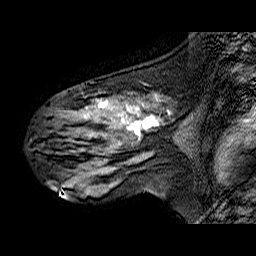
Breast MRI (dynamic contrast-enhanced), one sagittal slice. Slice 36 of 60 in the series (ordered by position). Dynamic contrast-enhanced series, time point 2 of 6 at this slice position (early post-contrast). 1.5 T. TE 6.3 ms, TR 32.9 ms. 4 mm slice thickness. 256 × 256 image matrix. Female patient. From the clinical record (not read from this slice): setting: breast cancer imaged before/during neoadjuvant chemotherapy; receptor status: HER2-positive.
Outlined on this slice (semi-automatic segmentation, software-assisted and operator-edited):
- analysis volume of interest (the breast-tissue region the enhancement analysis was run in; not a lesion): bounding box [x1, y1, x2, y2] px = [34, 90, 174, 173]
- tumour enhancement mask (voxels above the 100 % enhancement threshold inside the analysis volume of interest): [97, 100, 160, 143]